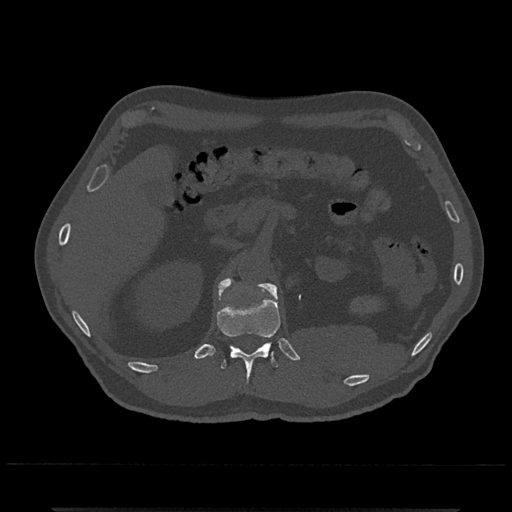
CT including the spine, one axial slice; position 417 of 797 along the scan axis; bone window (W 1800 / L 400 HU); 0.5 mm slice thickness; 512 × 512 image matrix, field of view 393 × 393 mm. Patient: male, 67 years. From the clinical record (not read from this slice): primary cancer: prostate.
Outlined on this slice (semi-automatically segmented with operator editing):
- L1 vertebra: box from (x=218, y=279) to (x=277, y=299) px
- T12 vertebra: (x=217, y=279)–(x=281, y=392)